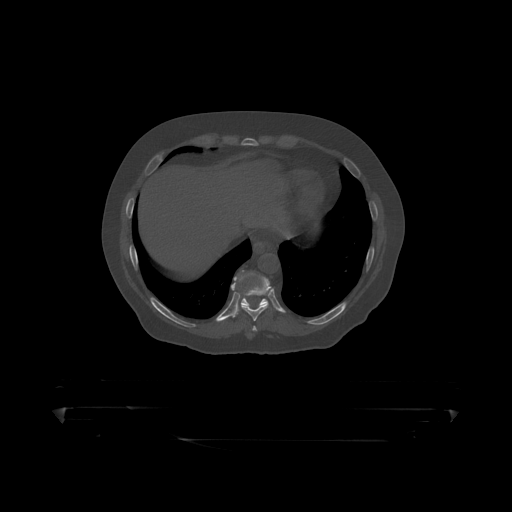
CT including the spine, one axial slice; slice 230 of 390 in the series (ordered by position); 120 kVp; bone window (W 1800 / L 400 HU); 1.25 mm slice thickness; 512 × 512 image matrix. Male patient, age 60 years. Case-level facts recorded for this patient, not image findings: primary cancer: prostate.
Outlined on this slice (semi-automatic segmentation, software-assisted and operator-edited):
- T10 vertebra: bounding box (x1, y1, x2, y2) in pixels: (235, 274, 268, 306)
- T9 vertebra: (232, 271, 271, 319)